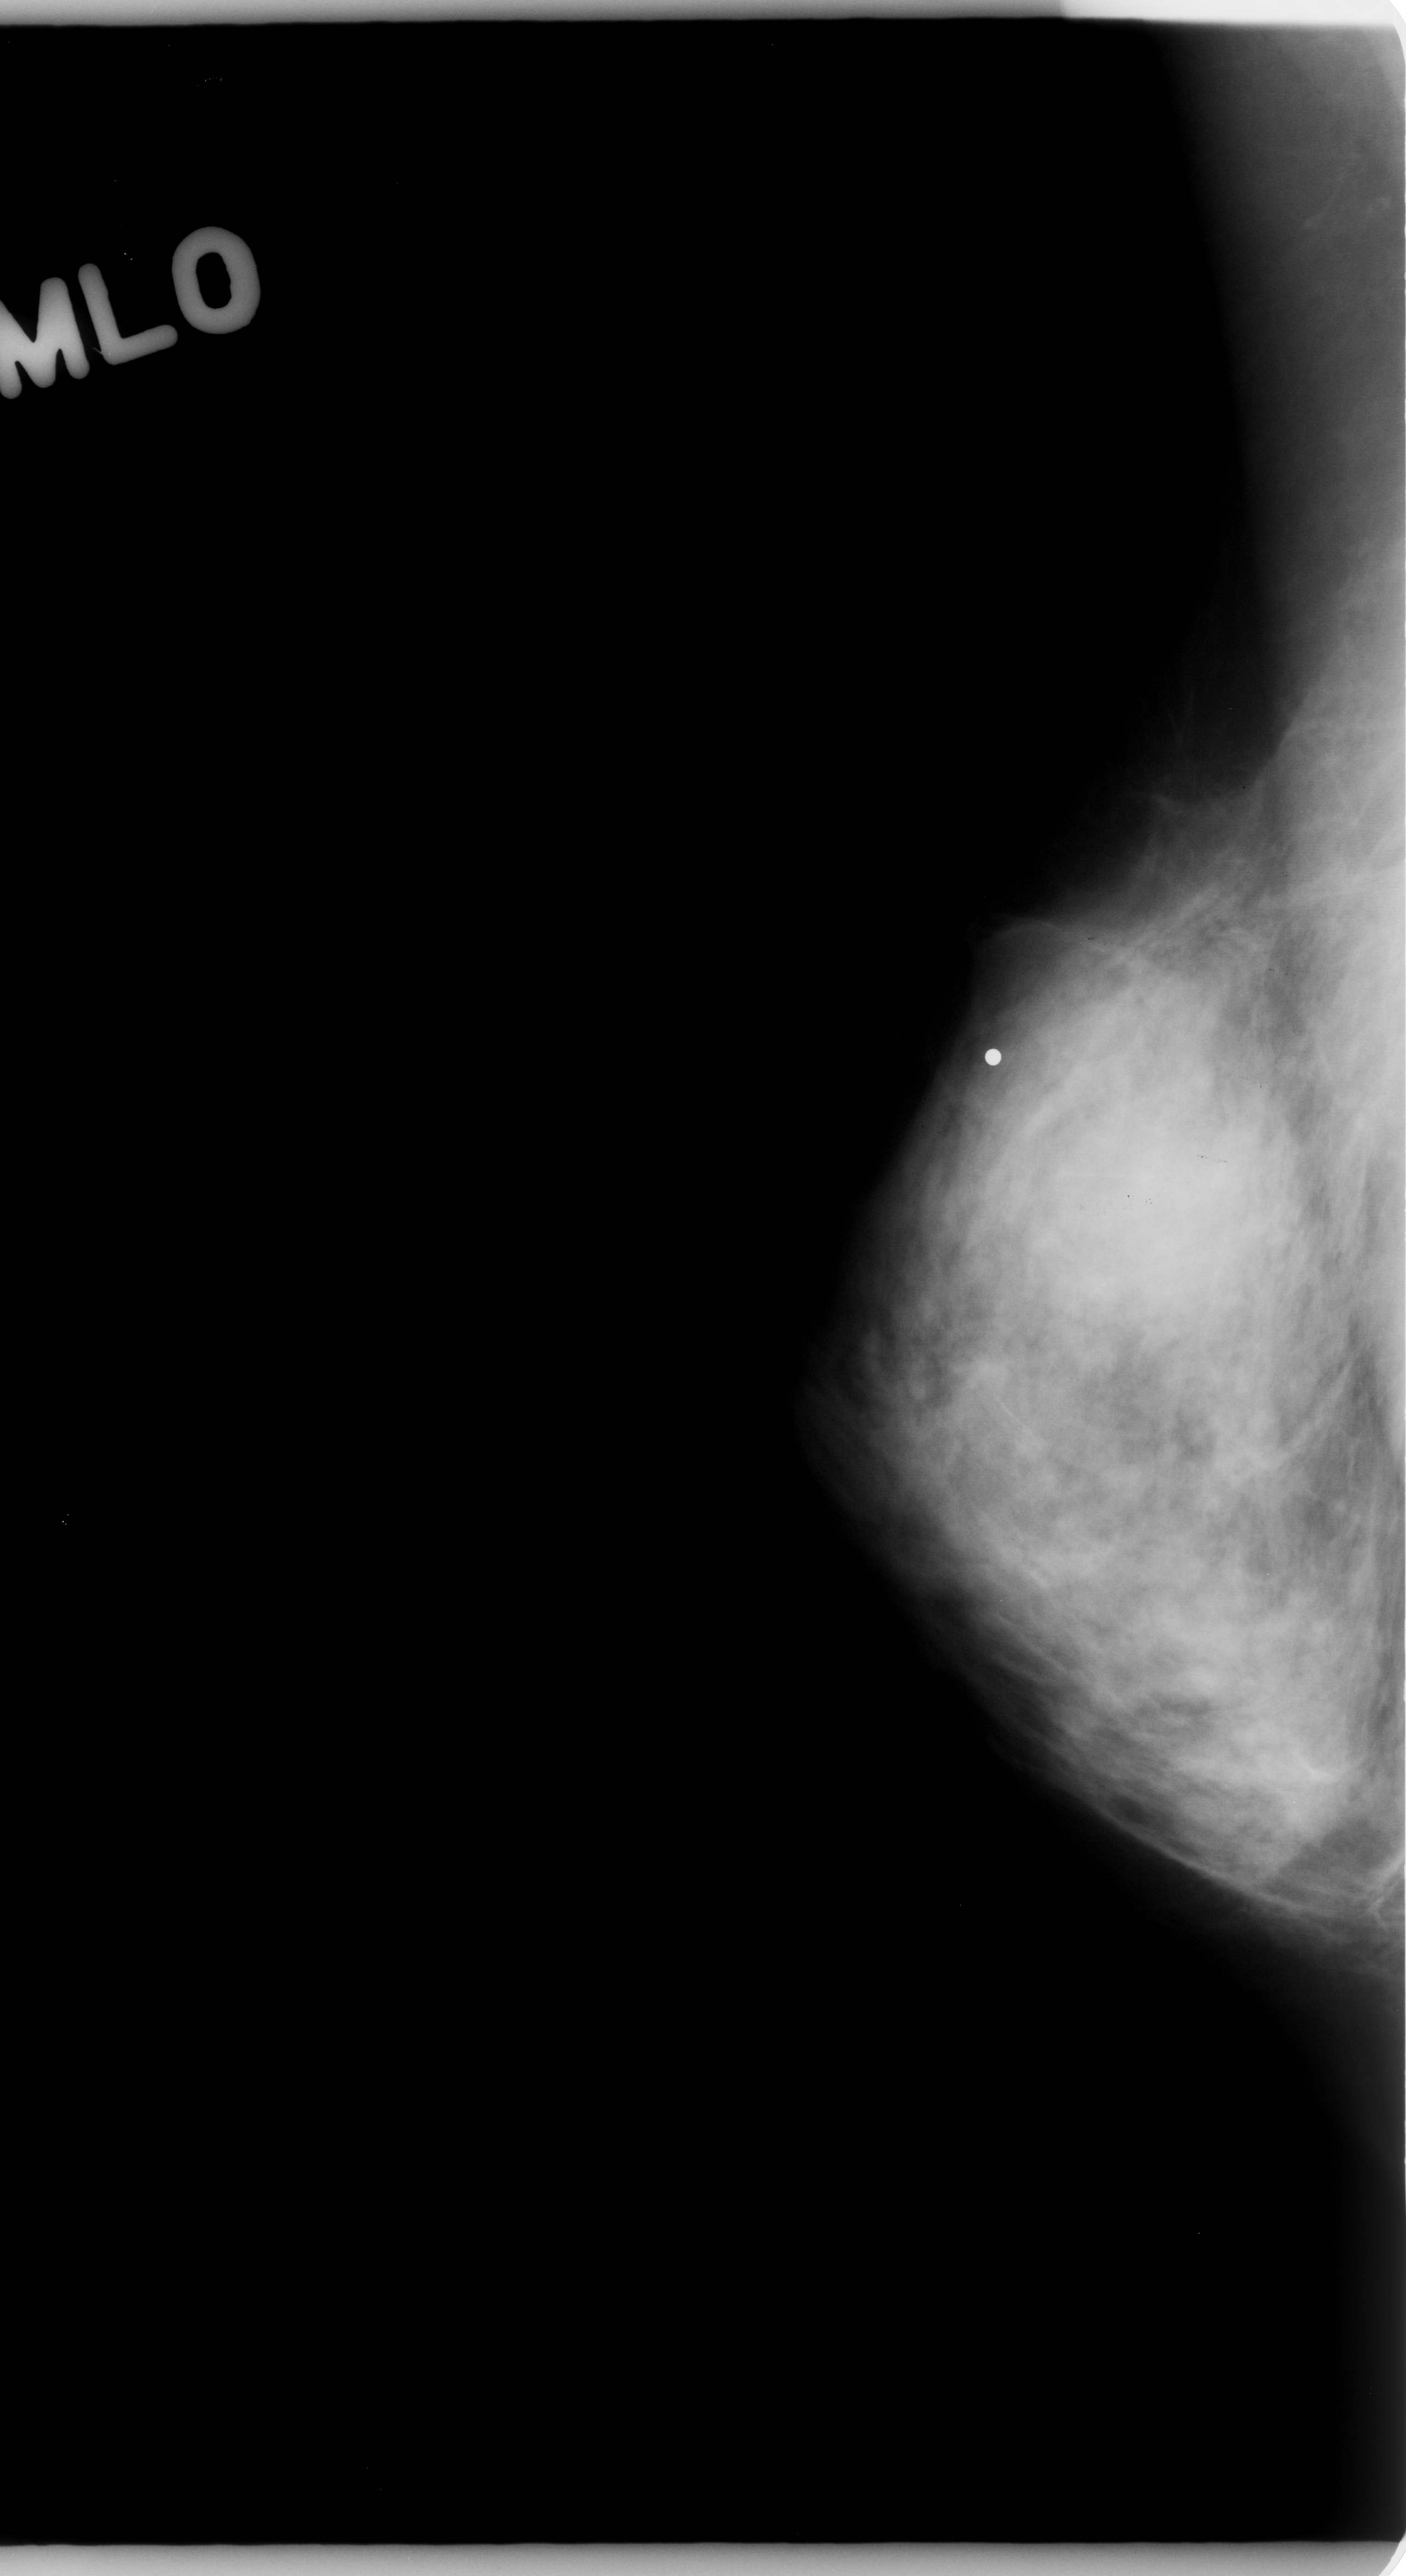
Digitized screen-film mammogram. Right breast. MLO view. BI-RADS breast density category 3 (scale 1–4). 1406 × 2576 image matrix.
Expert-marked regions of interest on this film, with their recorded descriptors:
- mass, shape round, margins ill defined; BI-RADS assessment category 4; pathology result (as recorded, not read from the image): malignant: box from (x=1056, y=1079) to (x=1305, y=1366) px